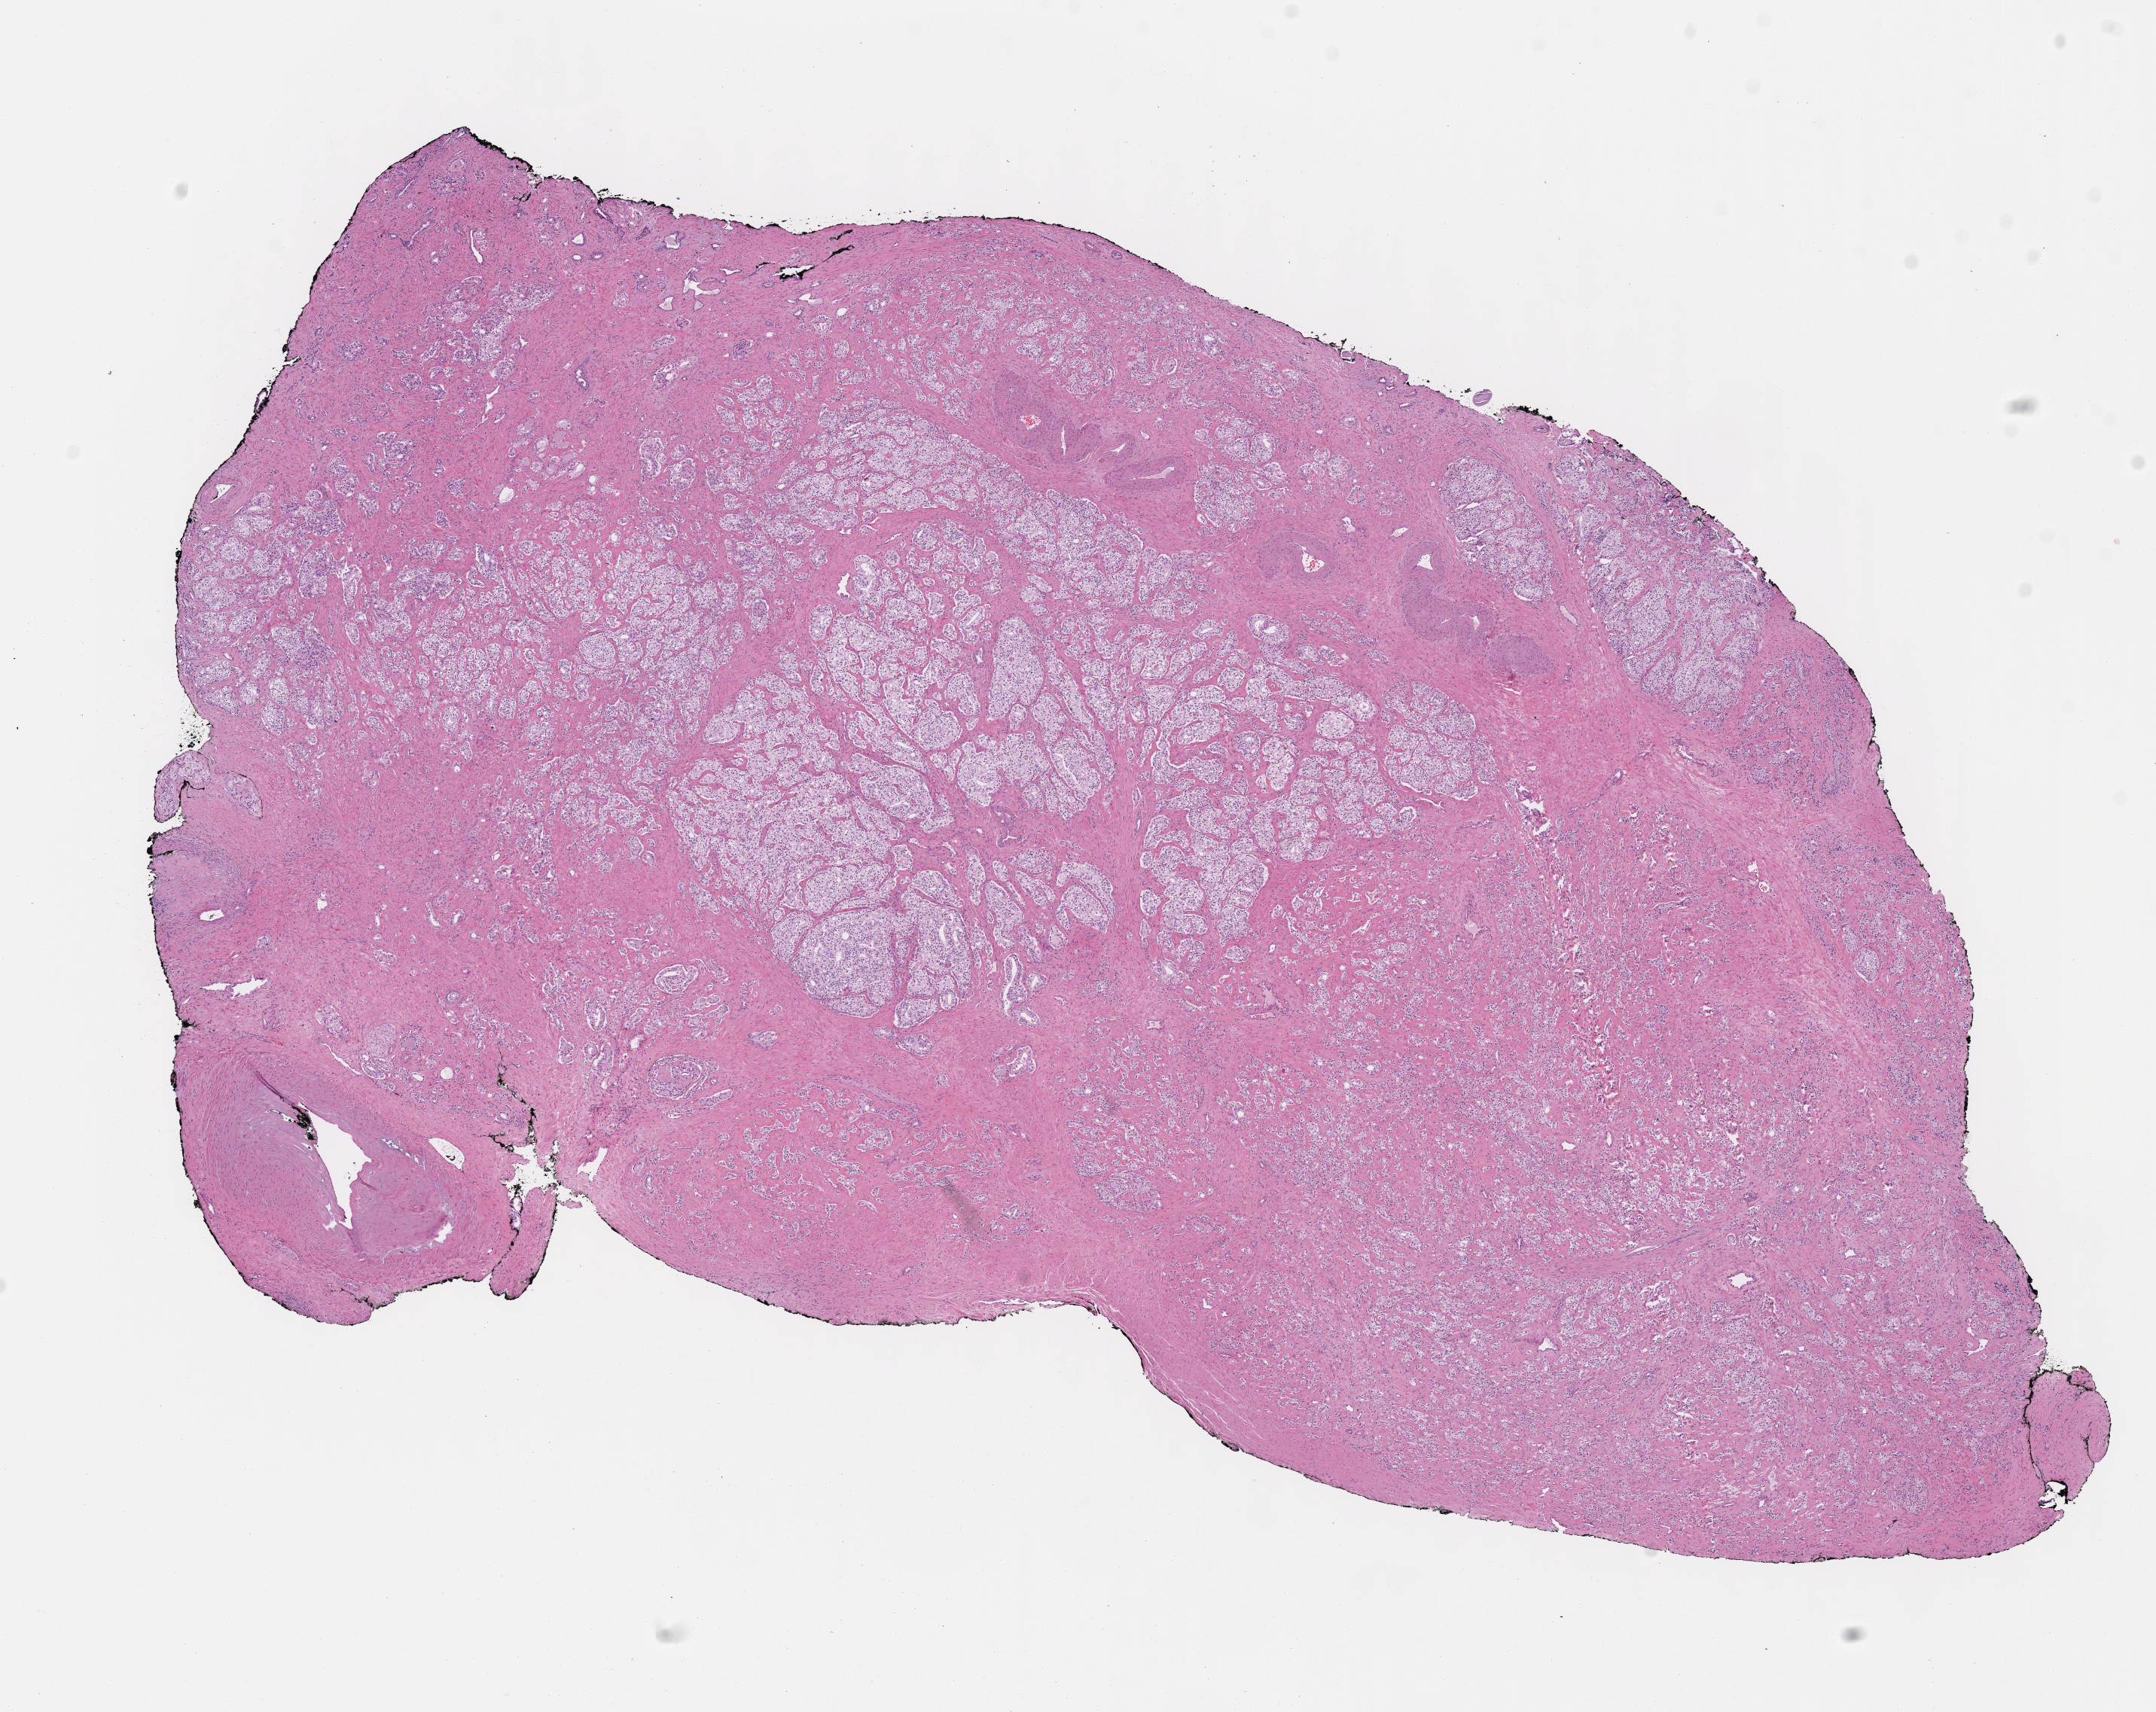
Whole-slide histology image, H&E-stained — shown as a low-resolution overview of the whole scanned area (about 11.3 x 8.9 mm, from a 40x scan); FFPE section; primary tumour sample from the prostate. Male, age 67 years at initial diagnosis.
Diagnosis: Acinar cell carcinoma (prostate gland).